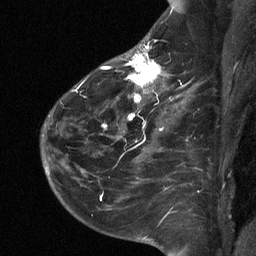
Breast MRI (dynamic contrast-enhanced), one sagittal slice; slice 44 of 64 in the series (ordered by position); dynamic contrast-enhanced study with each time point stored as its own series, time point 2 of 3 at this slice position (early post-contrast, ordered by acquisition time); 1.5 T; TE 4.8 ms, TR 27 ms; 256 × 256 image matrix, field of view 180 × 180 mm. Female patient, age 51 years. From the clinical record (not read from this slice): setting: breast cancer imaged before/during neoadjuvant chemotherapy; receptor status: HR-positive, HER2-negative.
Outlined on this slice (semi-automatically segmented with operator editing):
- analysis volume of interest (the breast-tissue region the enhancement analysis was run in; not a lesion): bounding box [x1, y1, x2, y2] px = [72, 34, 182, 118]
- tumour enhancement mask (voxels above the 90 % enhancement threshold inside the analysis volume of interest): [76, 44, 161, 118]